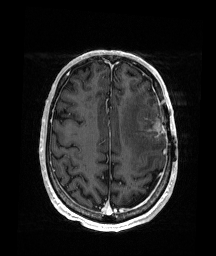
Brain MRI from a brain-tumour surgery series, one axial slice. T1-weighted post-contrast. 1 mm slice thickness. 216 × 256 image matrix. From the clinical record (not read from this slice): histopathology: Glioblastoma; WHO grade: 4; IDH mutation: no.
Structures marked on this image (outlined manually by an expert reader):
- tumour: bounding box [x1, y1, x2, y2] px = [140, 117, 165, 136]